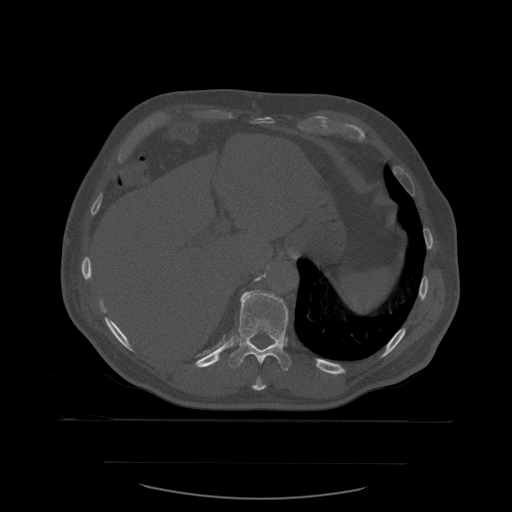
CT including the spine, one axial slice. Position 298 of 590 along the scan axis. Bone window (W 1800 / L 400 HU). 1.25 mm slice thickness. 512 × 512 image matrix. Patient age 71 years. From the clinical record (not read from this slice): primary cancer: lung.
Structures marked on this image (semi-automatically segmented with operator editing):
- T10 vertebra: box from (x=252, y=377) to (x=267, y=391) px
- T11 vertebra: (x=229, y=290)–(x=293, y=371)